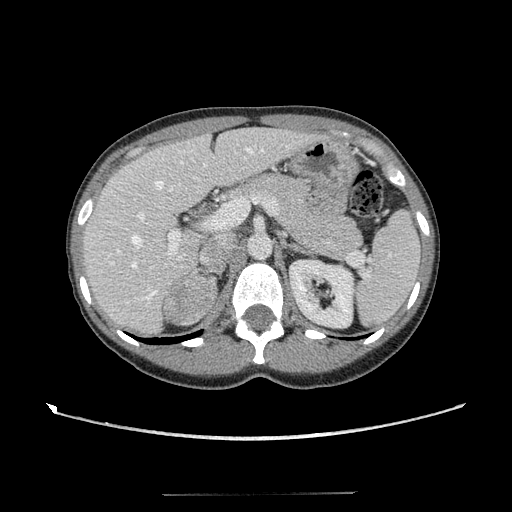
Contrast-enhanced abdominal CT, one axial slice; position 73 of 117 along the scan axis; reconstruction kernel STANDARD; 120 kVp; intravenous contrast given; soft-tissue window (W 400 / L 40 HU); 512 × 512 image matrix. Patient: female, 35 years. Case-level facts recorded for this patient, not image findings: diagnosis: adrenocortical carcinoma; tumour side: right adrenal; tumour size at pathology: 3 cm; Ki-67 index: 21 %; stage (as recorded): 3.
Annotated regions visible in this slice (semi-automatically segmented with operator editing):
- mass: bounding box [x1, y1, x2, y2] px = [164, 280, 215, 323]